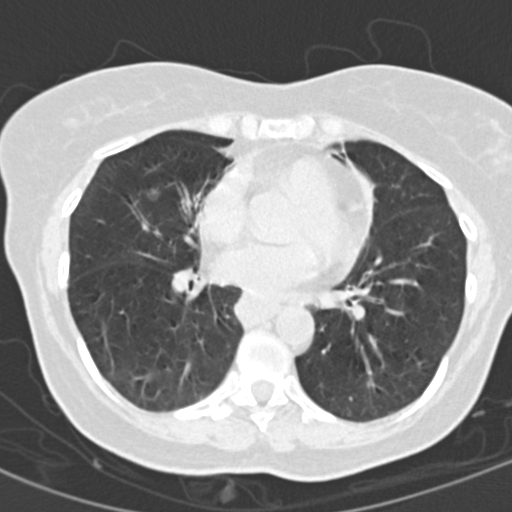
Low-dose screening chest CT, one axial slice; slice 69 of 154 in the series (ordered by position); lung window (W 1500 / L -600 HU); 512 × 512 image matrix.
Structures marked on this image (expert manual segmentation):
- lesion 1 (nodule, middle lobe of right lung): bounding box [x1, y1, x2, y2] px = [145, 187, 161, 201]